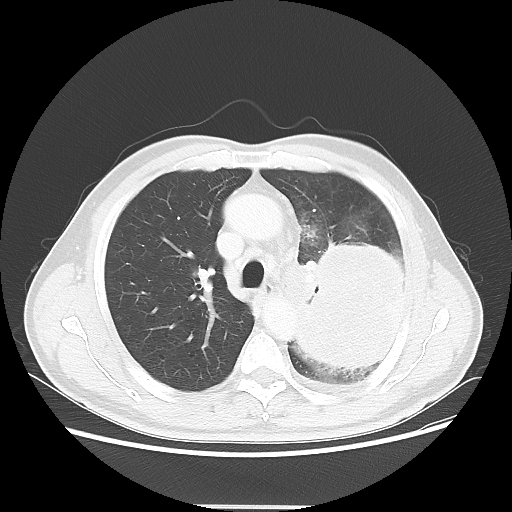
Chest CT, one axial slice; reconstruction kernel LUNG; 100 kVp; lung window (W 1500 / L -600 HU); 5 mm slice thickness; 512 × 512 image matrix, field of view 391 × 391 mm. Patient: male, 60 years. From the clinical record (not read from this slice): clinical TNM (as recorded): T4 N1 M1a.
Structures marked on this image (rectangle marked by the reading radiologist):
- lung tumour (recorded histology: large cell carcinoma): box from (x=289, y=231) to (x=409, y=382) px